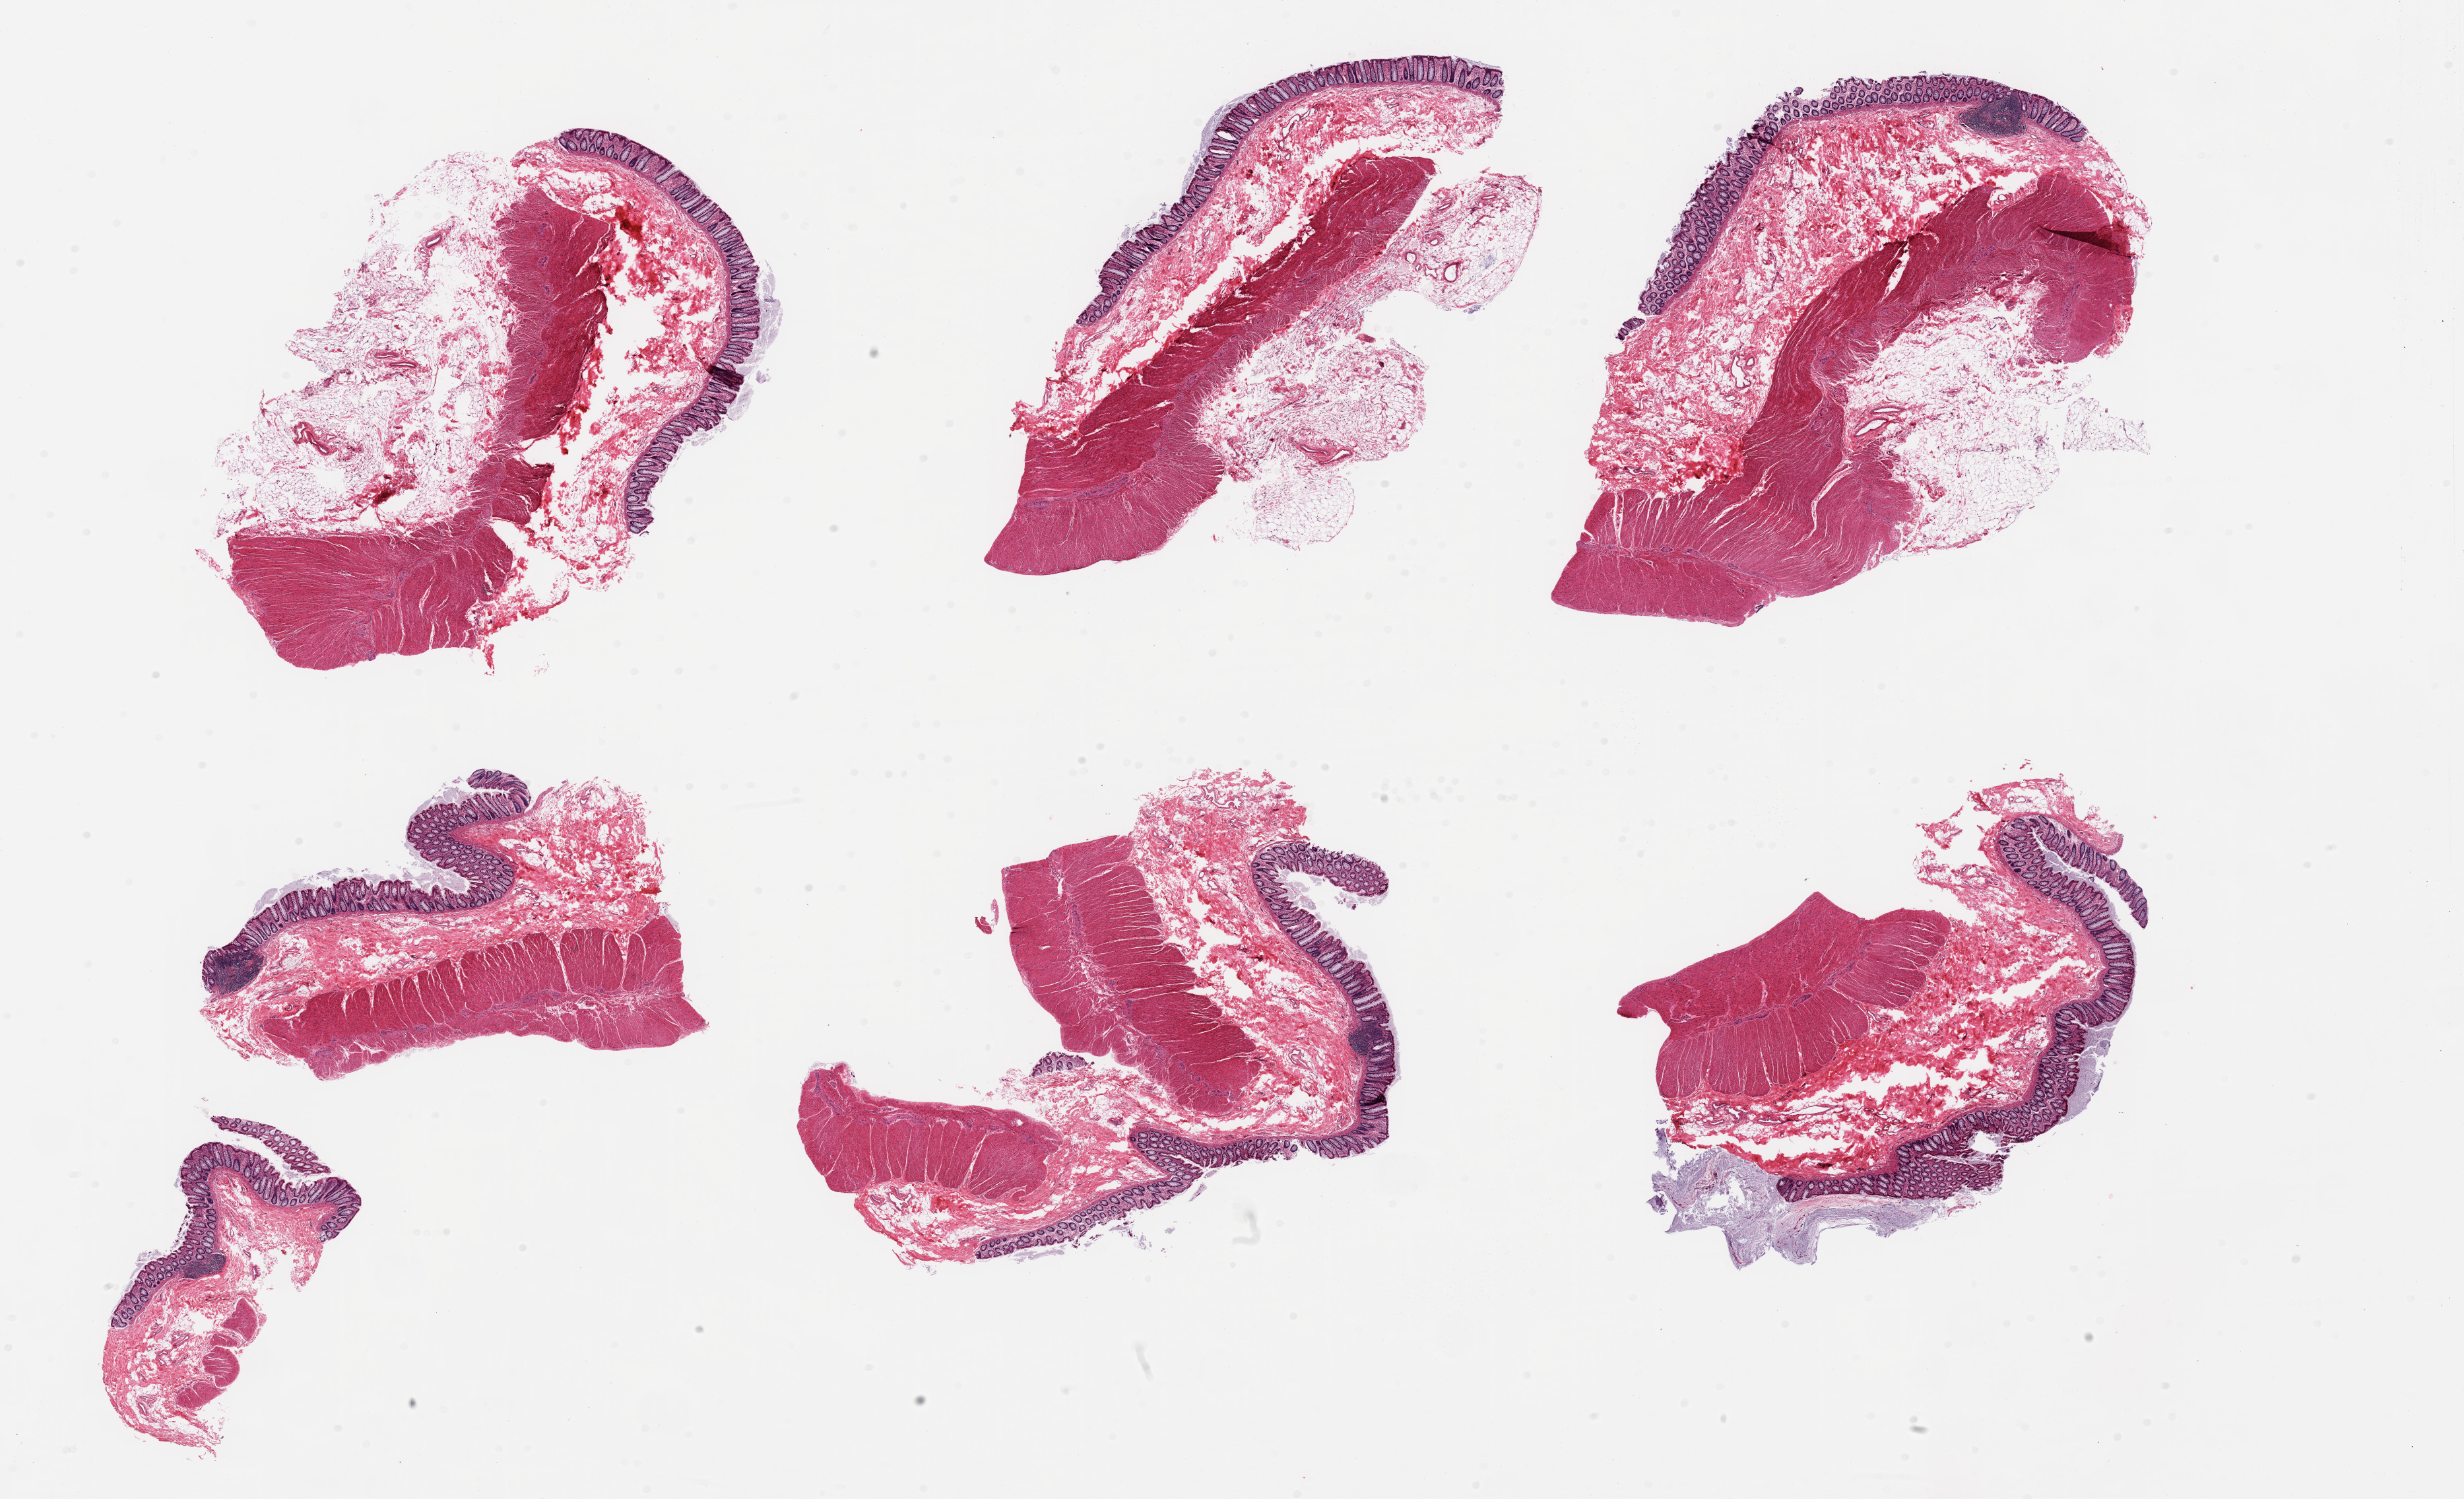
Digitized hematoxylin and eosin (H&E)-stained section, whole scanned area (about 29.5 x 18.0 mm) shown as a low-resolution overview; PAXgene-fixed, paraffin-embedded tissue; target tissue: sigmoid colon; tissue donor sample. Donor: female.
Pathologist's review note for this sample: 6 pieces, ~target muscularis, ~50% of tissue, rest is 'contaminant' serosa/mucosa.